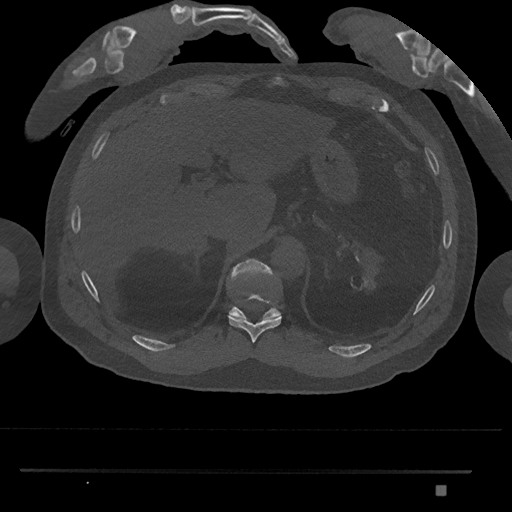
CT including the spine, one axial slice. Position 983 of 1134 along the scan axis. 120 kVp. Bone window (W 1800 / L 400 HU). 512 × 512 image matrix, field of view 429 × 429 mm. Patient: male, 65 years. Case-level facts recorded for this patient, not image findings: primary cancer: prostate.
Annotated regions visible in this slice (semi-automatic segmentation, software-assisted and operator-edited):
- T10 vertebra: box from (x=228, y=295) to (x=282, y=343) px
- T11 vertebra: (x=226, y=259)–(x=281, y=320)